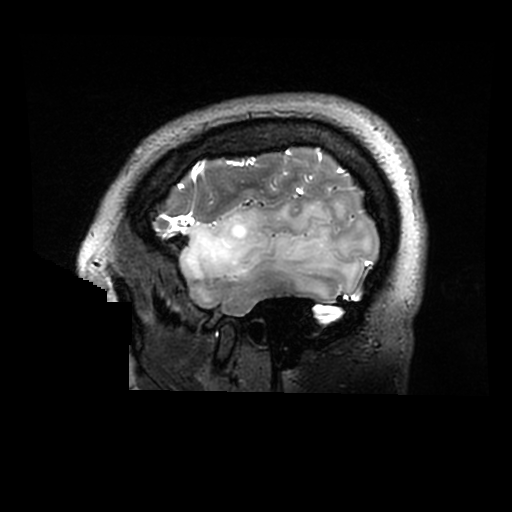
Brain MRI from a brain-tumour surgery series, one sagittal slice. Position 242 of 320 along the scan axis. 512 × 512 image matrix, field of view 240 × 240 mm. From the clinical record (not read from this slice): histopathology: Astrocytoma; WHO grade: 2; IDH mutation: yes.
Annotated regions visible in this slice (expert manual segmentation):
- tumour: bounding box <179,201,363,299> (left, top, right, bottom; pixels)